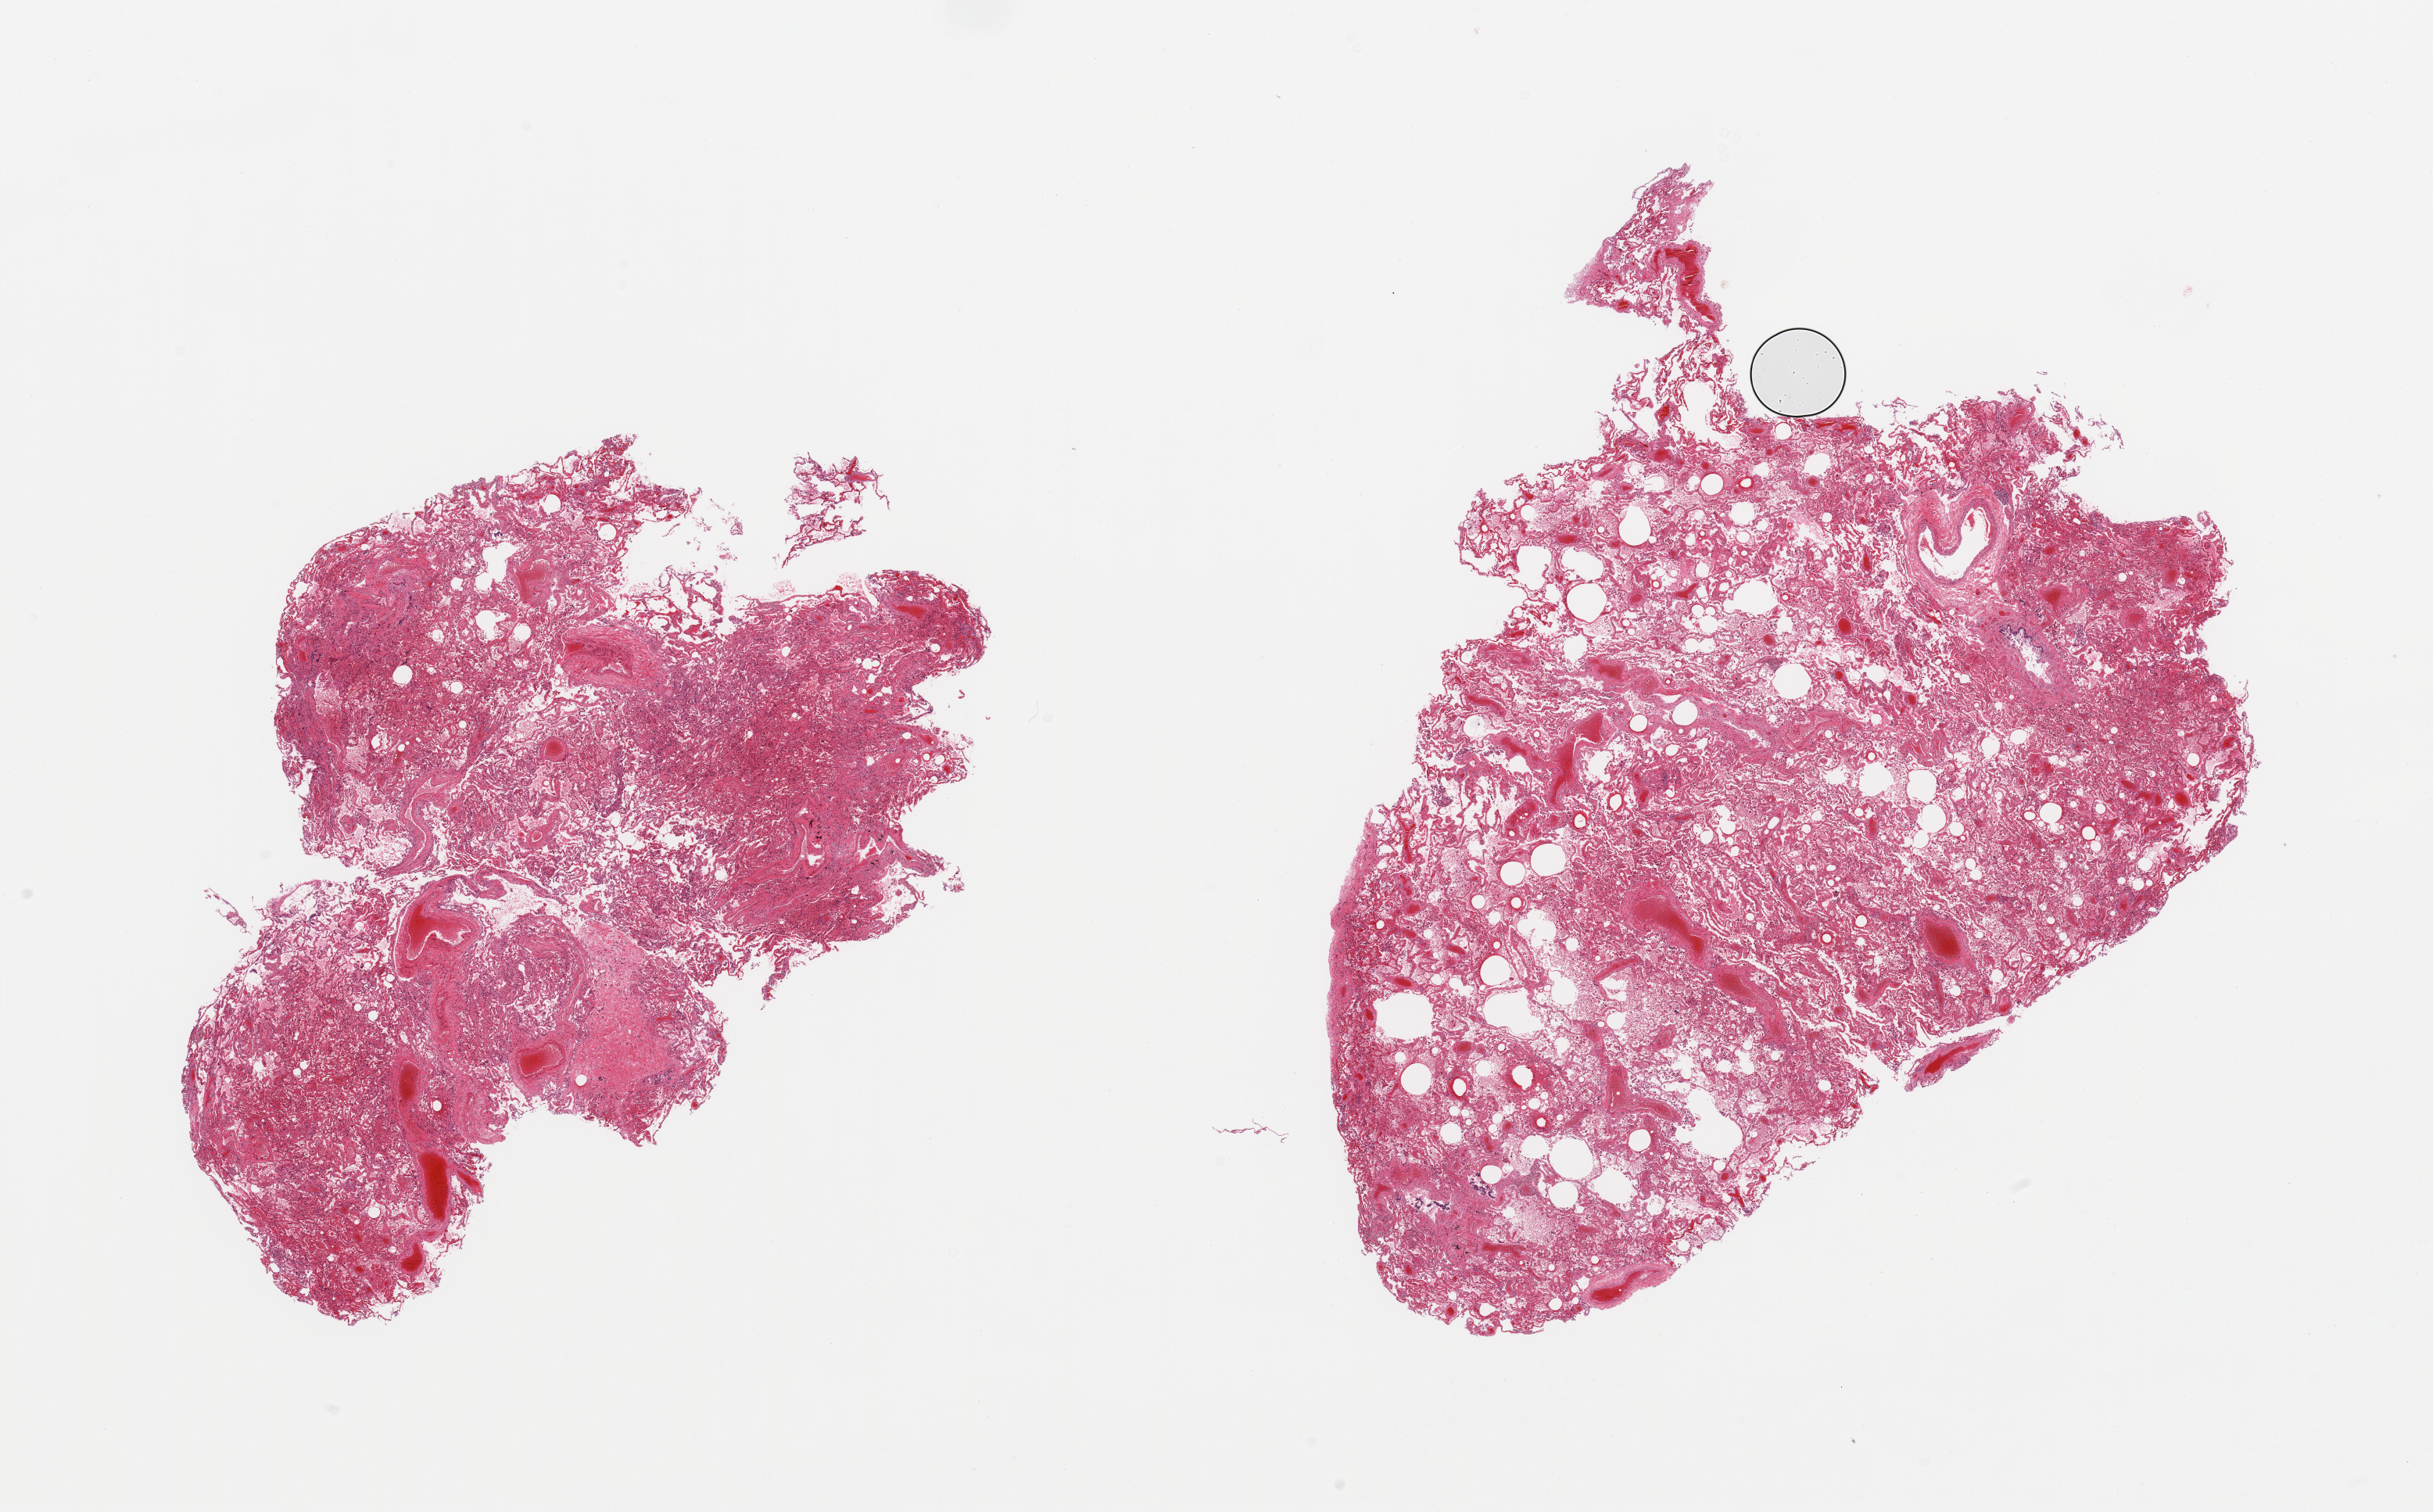
Hematoxylin and eosin (H&E) whole-slide image — shown as a low-resolution overview of the whole scanned area (about 24.6 x 15.3 mm). PAXgene-fixed paraffin-embedded (PFPE) section. Sampled site (target tissue): lung. Tissue donor sample. Donor sex: male.
Reviewer comment on this tissue sample: 2 pieces, moderate congestion.